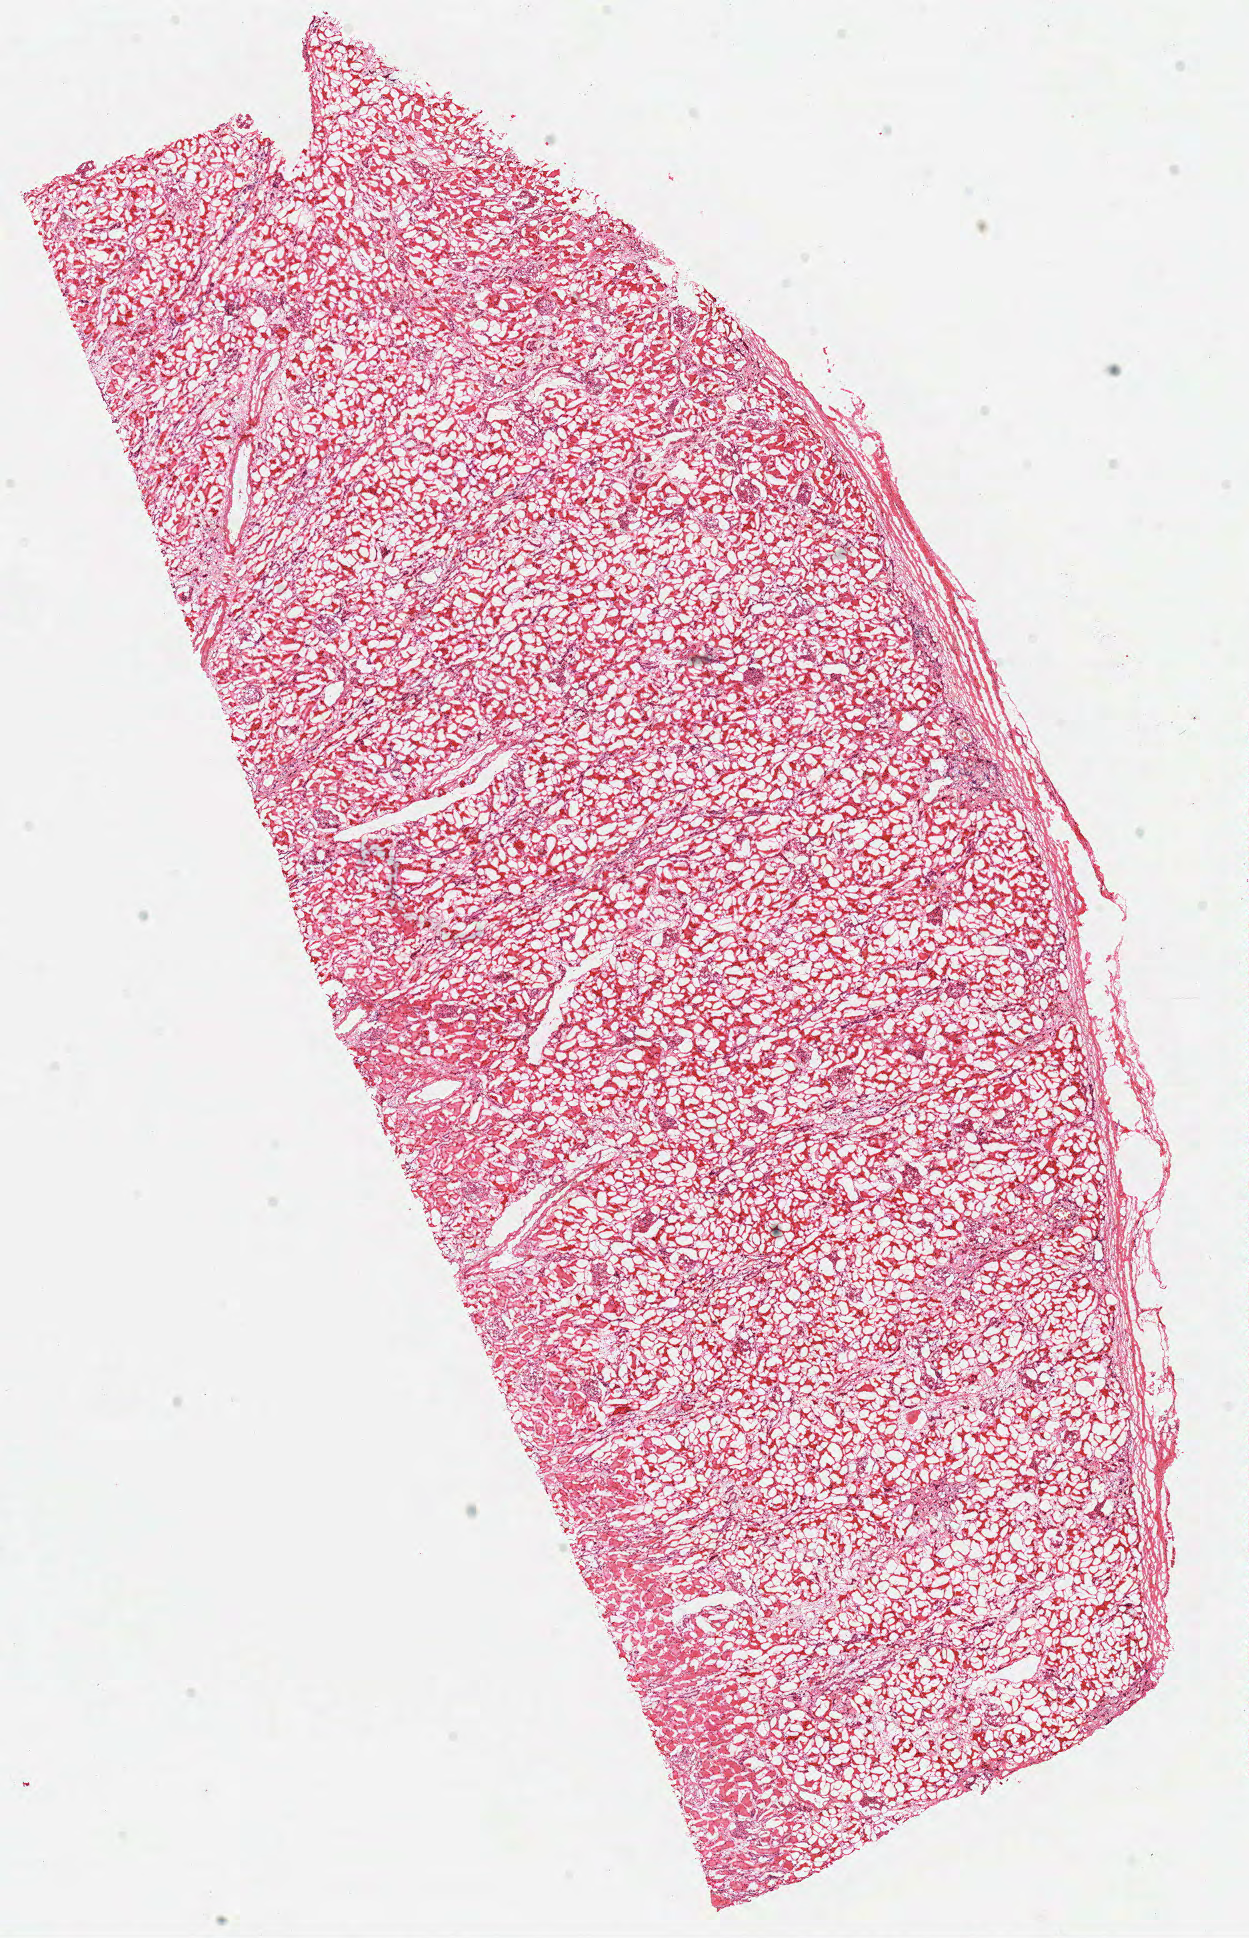
Digitized H&E tissue section (whole slide), a low-resolution overview of the entire scanned area, about 9.8 x 15.3 mm (acquisition: 40x scan). Frozen section from the top of the tissue portion. Solid tissue normal (non-tumour tissue) sample from the kidney. Male, age 51 years at initial diagnosis.
- this section: solid tissue normal sample (biorepository sample class)
- patient diagnosis: Clear cell adenocarcinoma, NOS